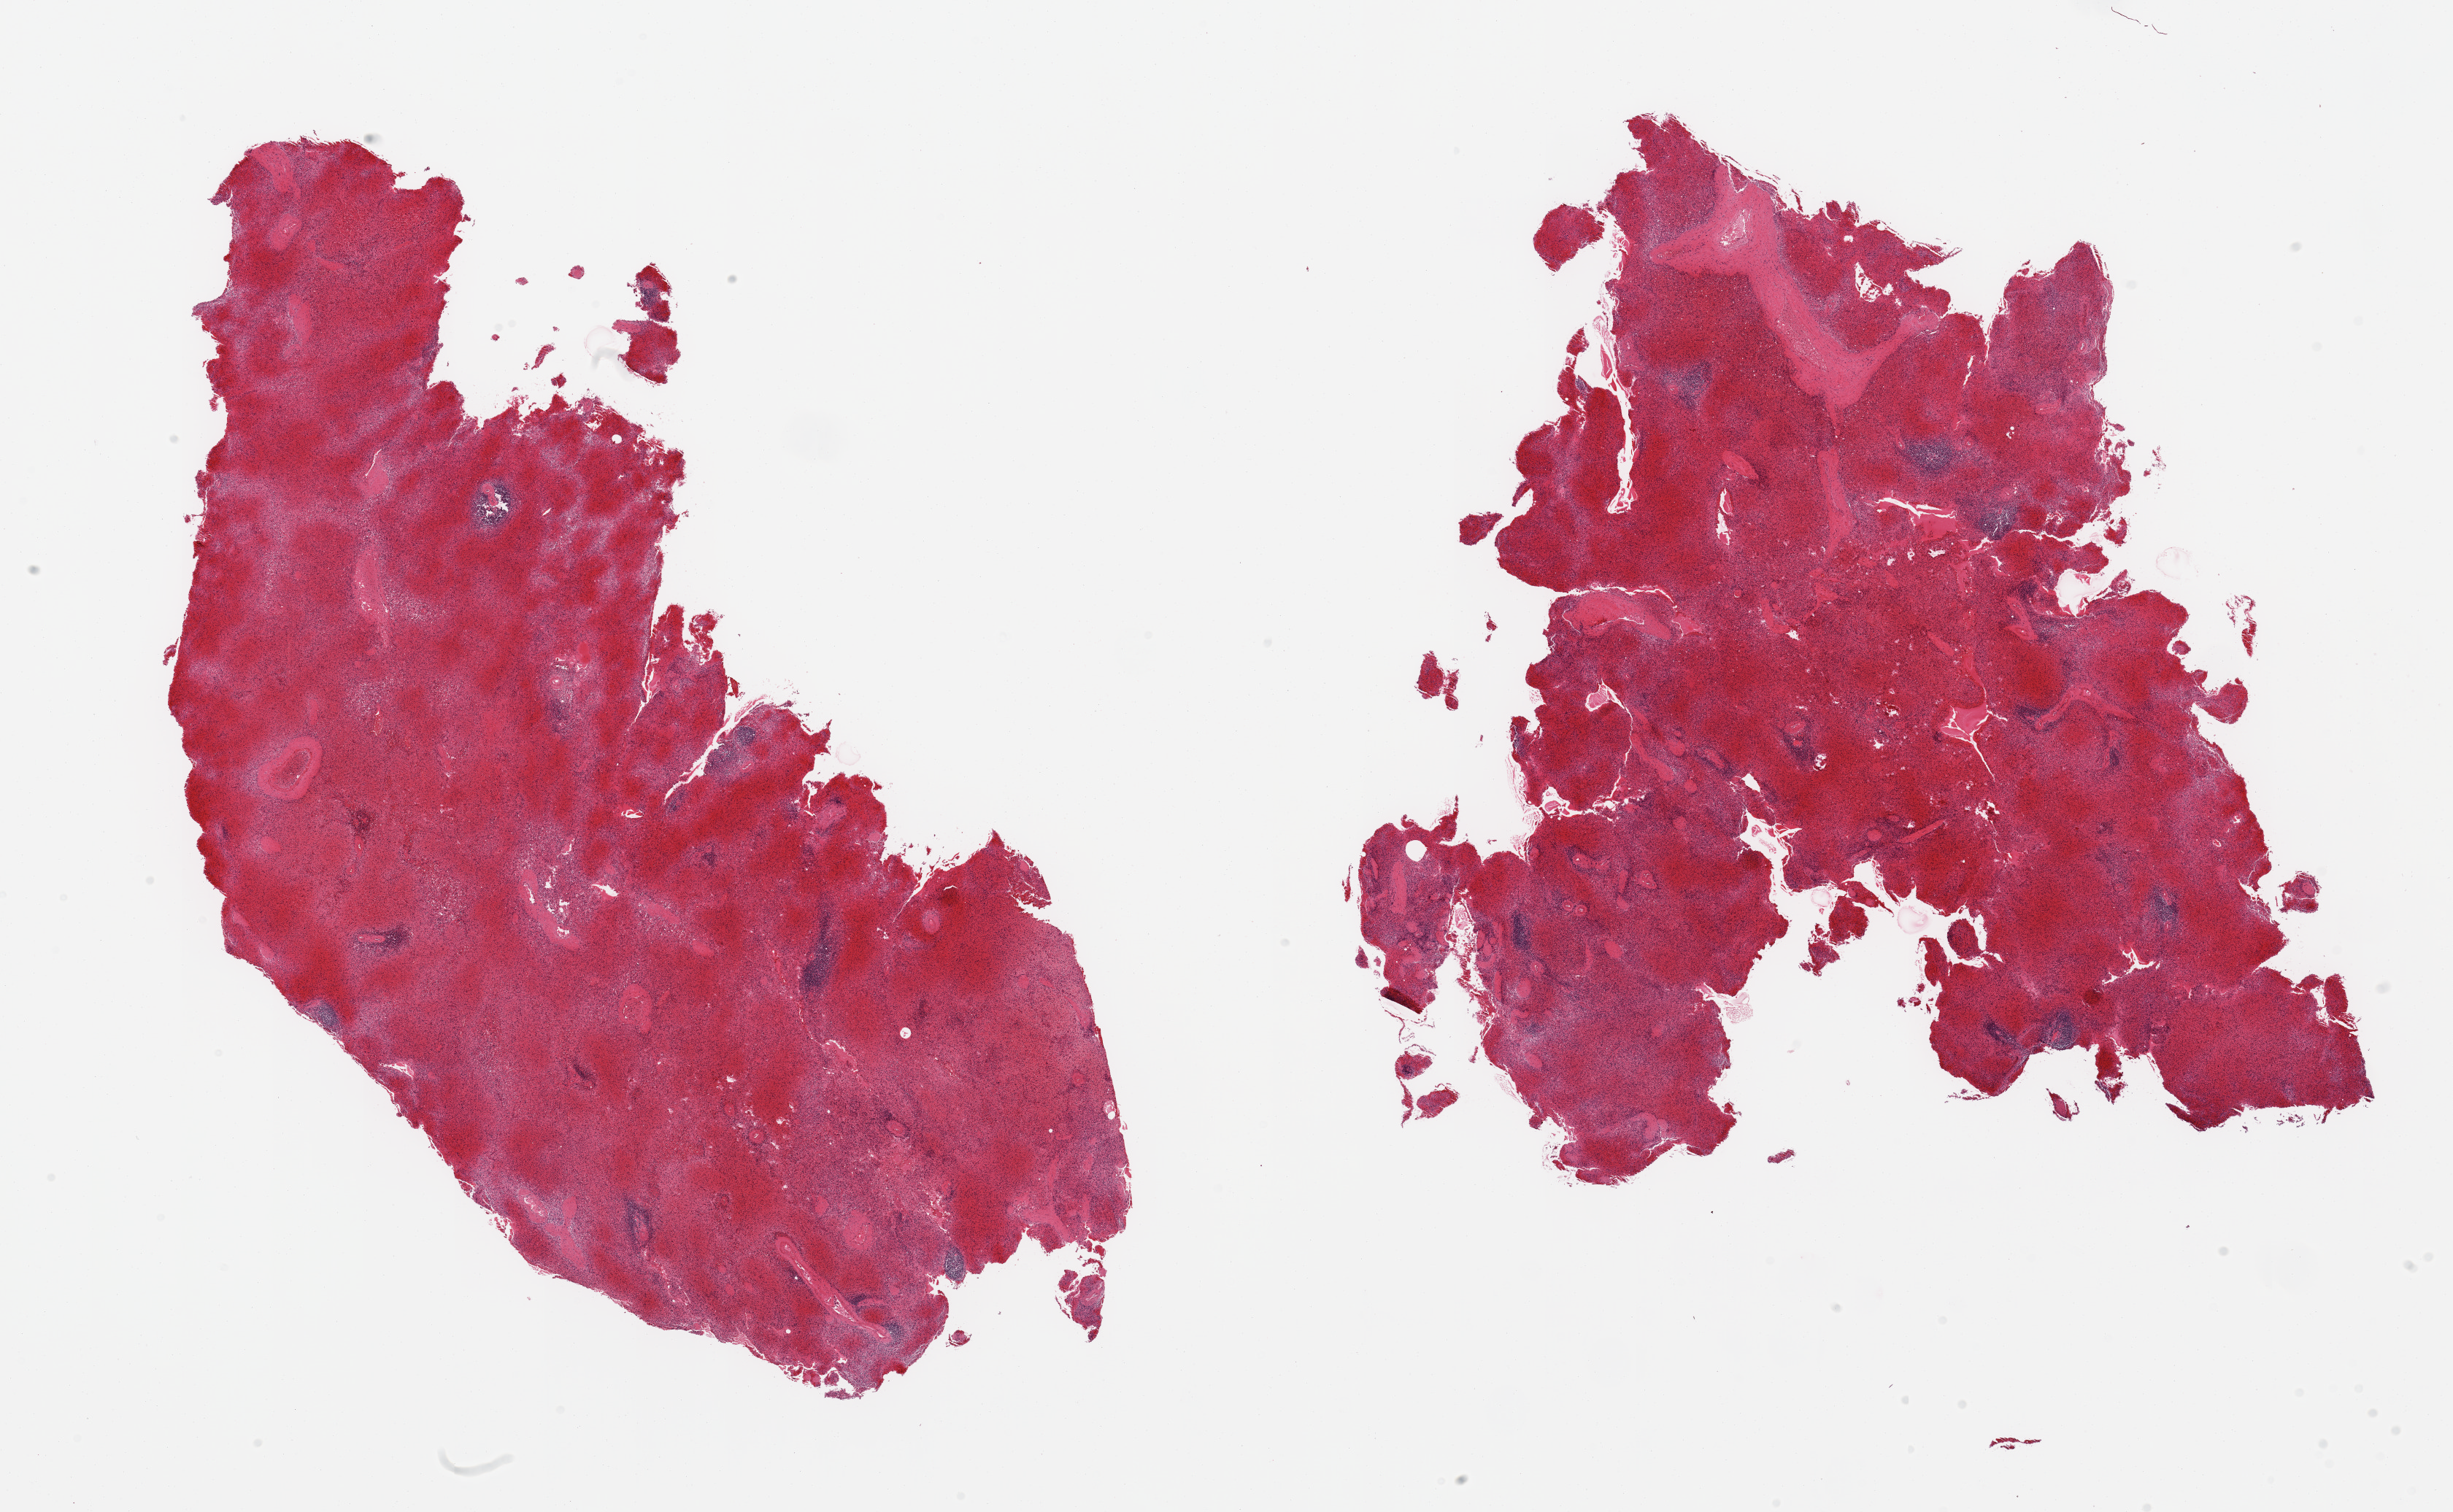
Digitized H&E-stained section, a low-resolution overview of the entire scanned area, about 26.6 x 16.4 mm (acquisition: 20x scan), PAXgene-fixed, paraffin-embedded tissue, section of spleen (target tissue), donor tissue sample. Donor sex: male.
Reviewer comment on this tissue sample: 2 pieces, marked congestion.